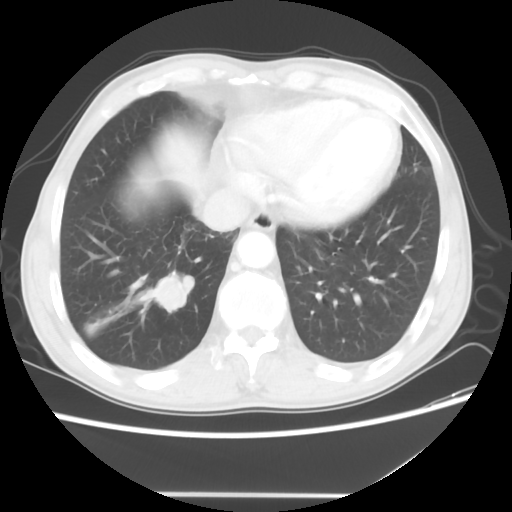
Chest CT, one axial slice. Position 12 of 56 along the scan axis. Lung window (W 1500 / L -600 HU). 512 × 512 image matrix, field of view 344 × 344 mm. Patient: male, 65 years. From the clinical record (not read from this slice): clinical TNM (as recorded): T1c N3 M0; histopathological grade: G3.
Outlined on this slice (rectangle marked by the reading radiologist):
- lung tumour (recorded histology: small cell carcinoma): box from (x=129, y=274) to (x=199, y=315) px